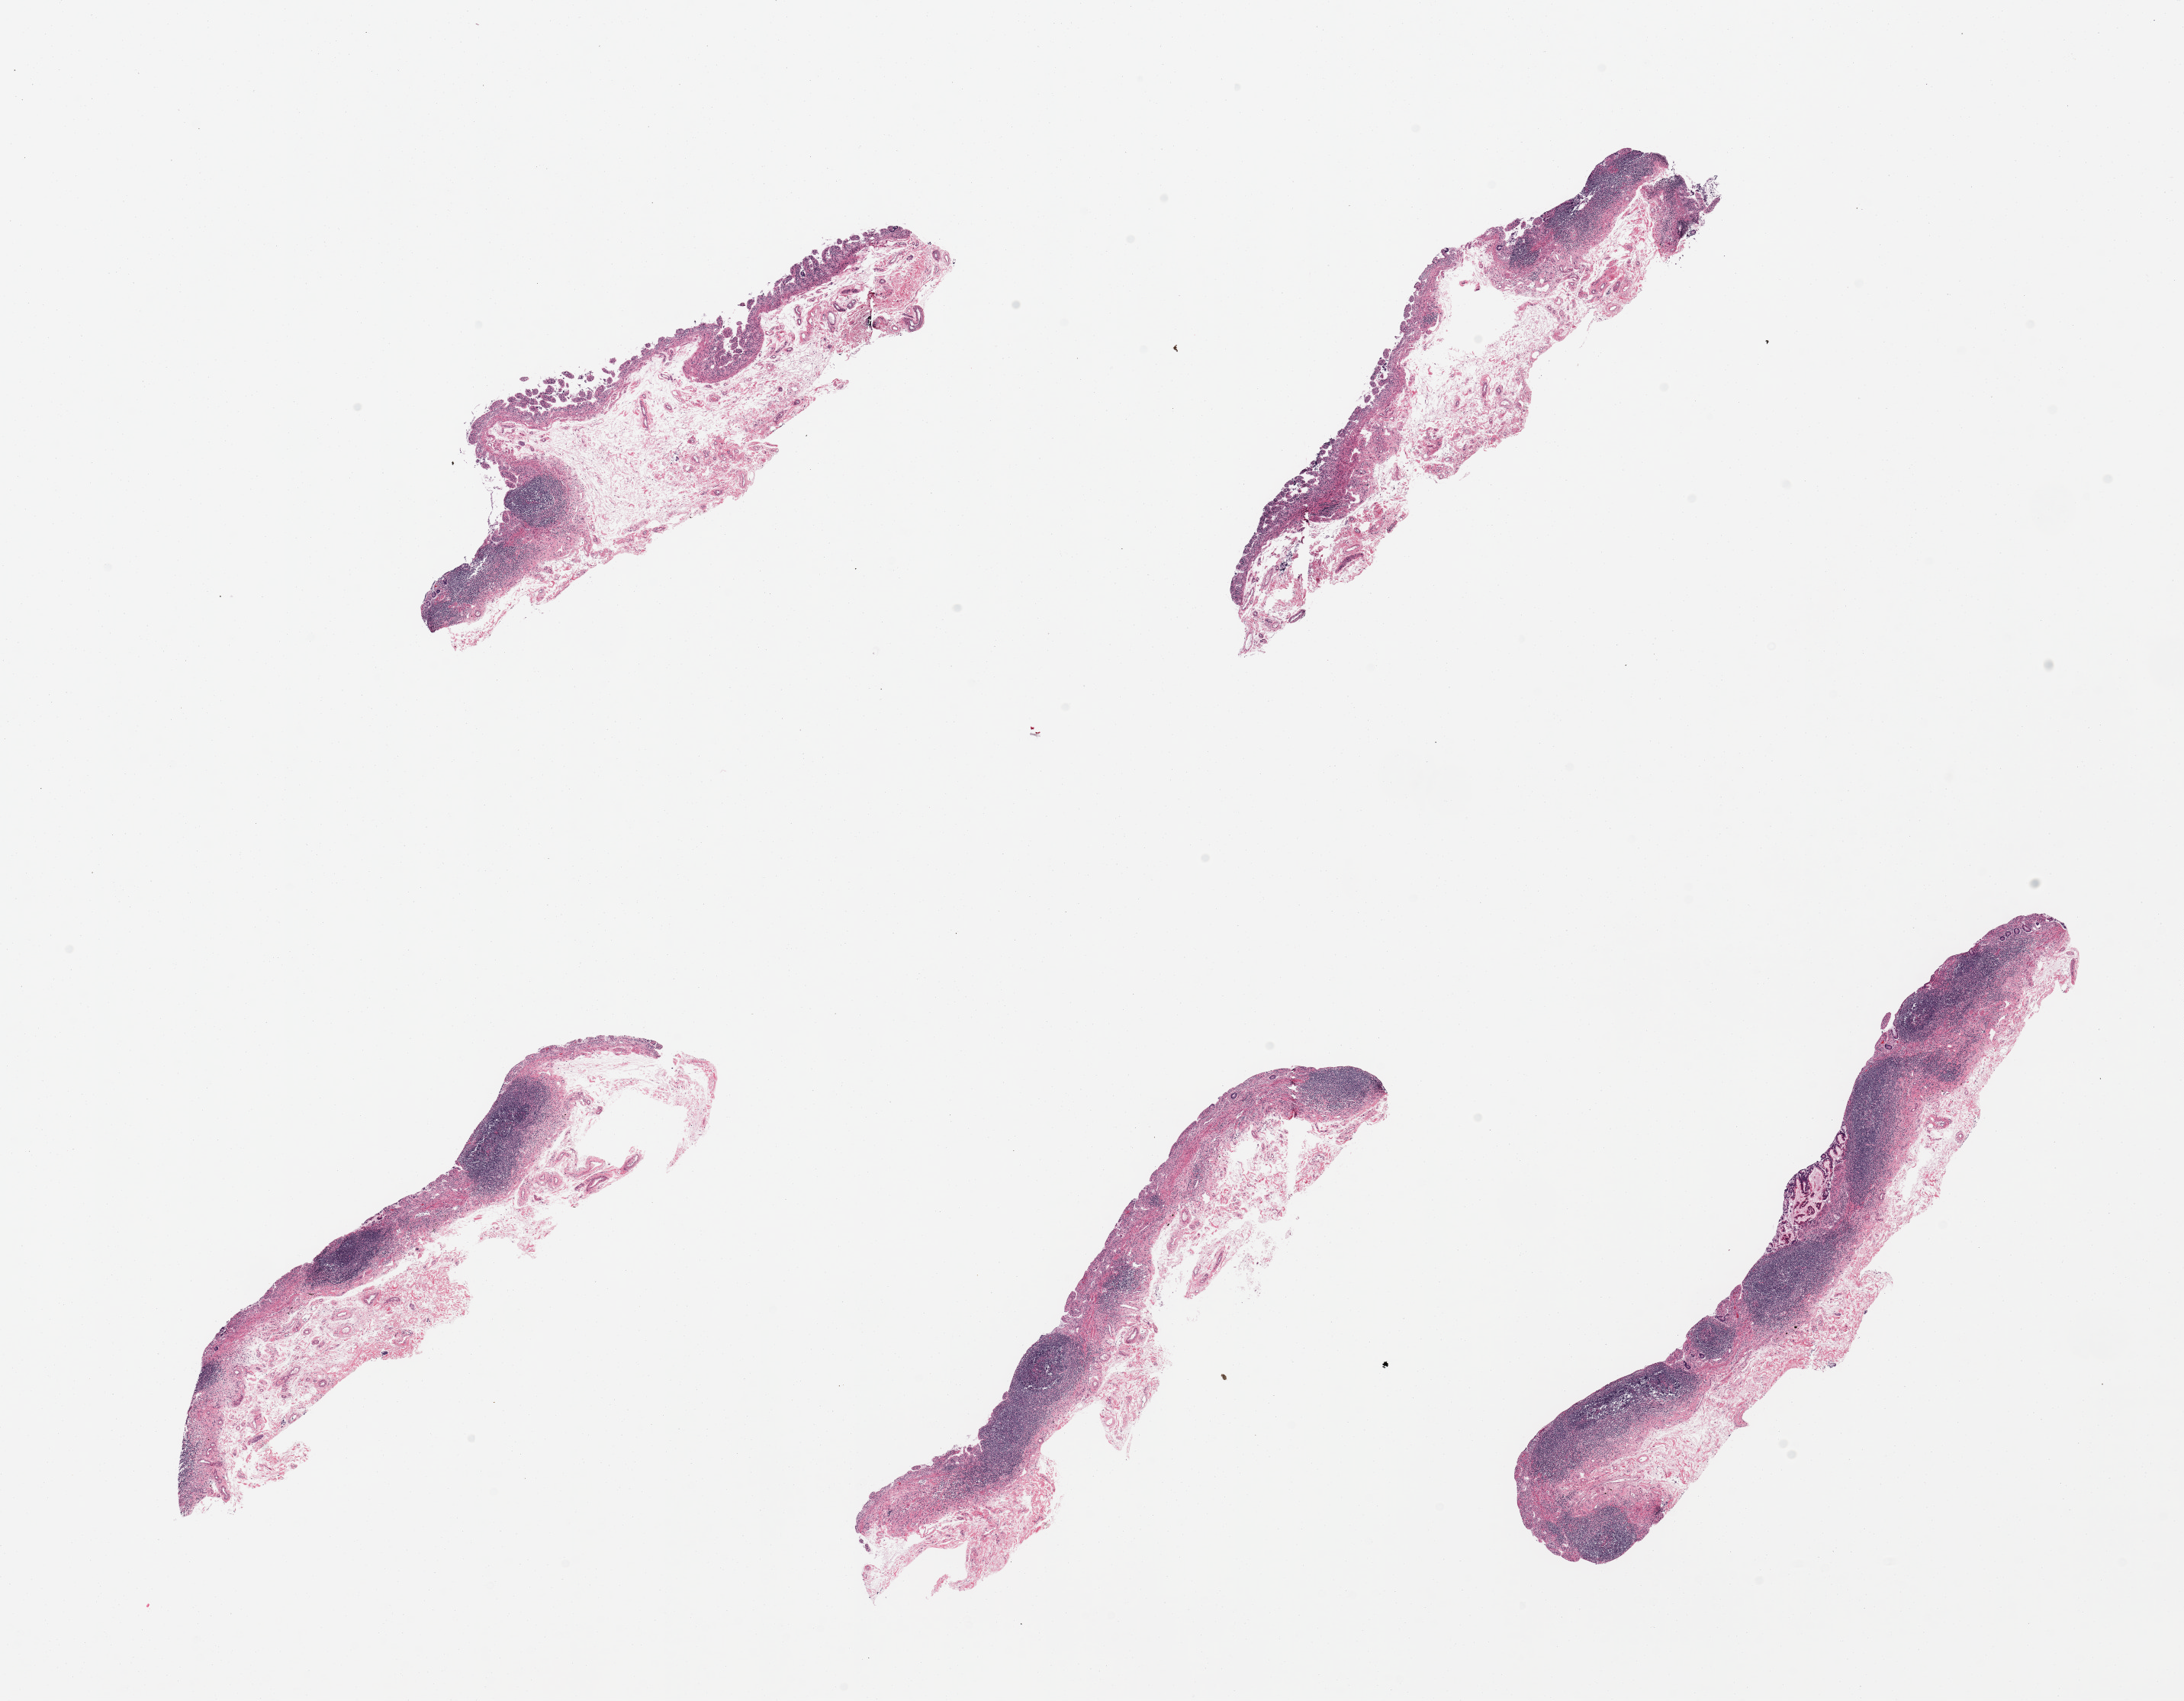
Digitized haematoxylin and eosin-stained section — low-resolution overview of the scanned area, about 22.6 x 17.6 mm, PAXgene-fixed paraffin-embedded (PFPE) section, sampled site (target tissue): ileum, donor tissue sample.
Pathologist's review note for this sample: 6 pieces, glandular elements of mucosa completely sloughed; residual lymphoid aggregates are ~25% residual tissue.